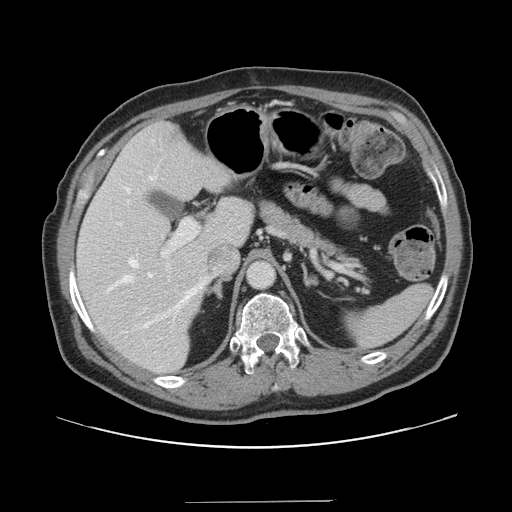
Contrast-enhanced abdominal CT, one axial slice. Slice 97 of 151 in the series (ordered by position). Intravenous contrast given. Soft-tissue window (W 400 / L 40 HU). 2.5 mm slice thickness. 512 × 512 image matrix. Male patient, age 63 years. From the clinical record (not read from this slice): diagnosis: colorectal cancer liver metastases, imaged before liver resection; multiple liver metastases: no; largest metastasis: 2.1 cm; chemotherapy before resection: no.
Annotated regions visible in this slice (manually delineated by an expert):
- hepatic veins: bounding box <108,176,209,333> (left, top, right, bottom; pixels)
- liver: <78,123,253,373>
- planned liver remnant (the part of the liver to remain after resection): <77,123,251,373>
- portal vein (with intrahepatic branches): <144,219,198,310>